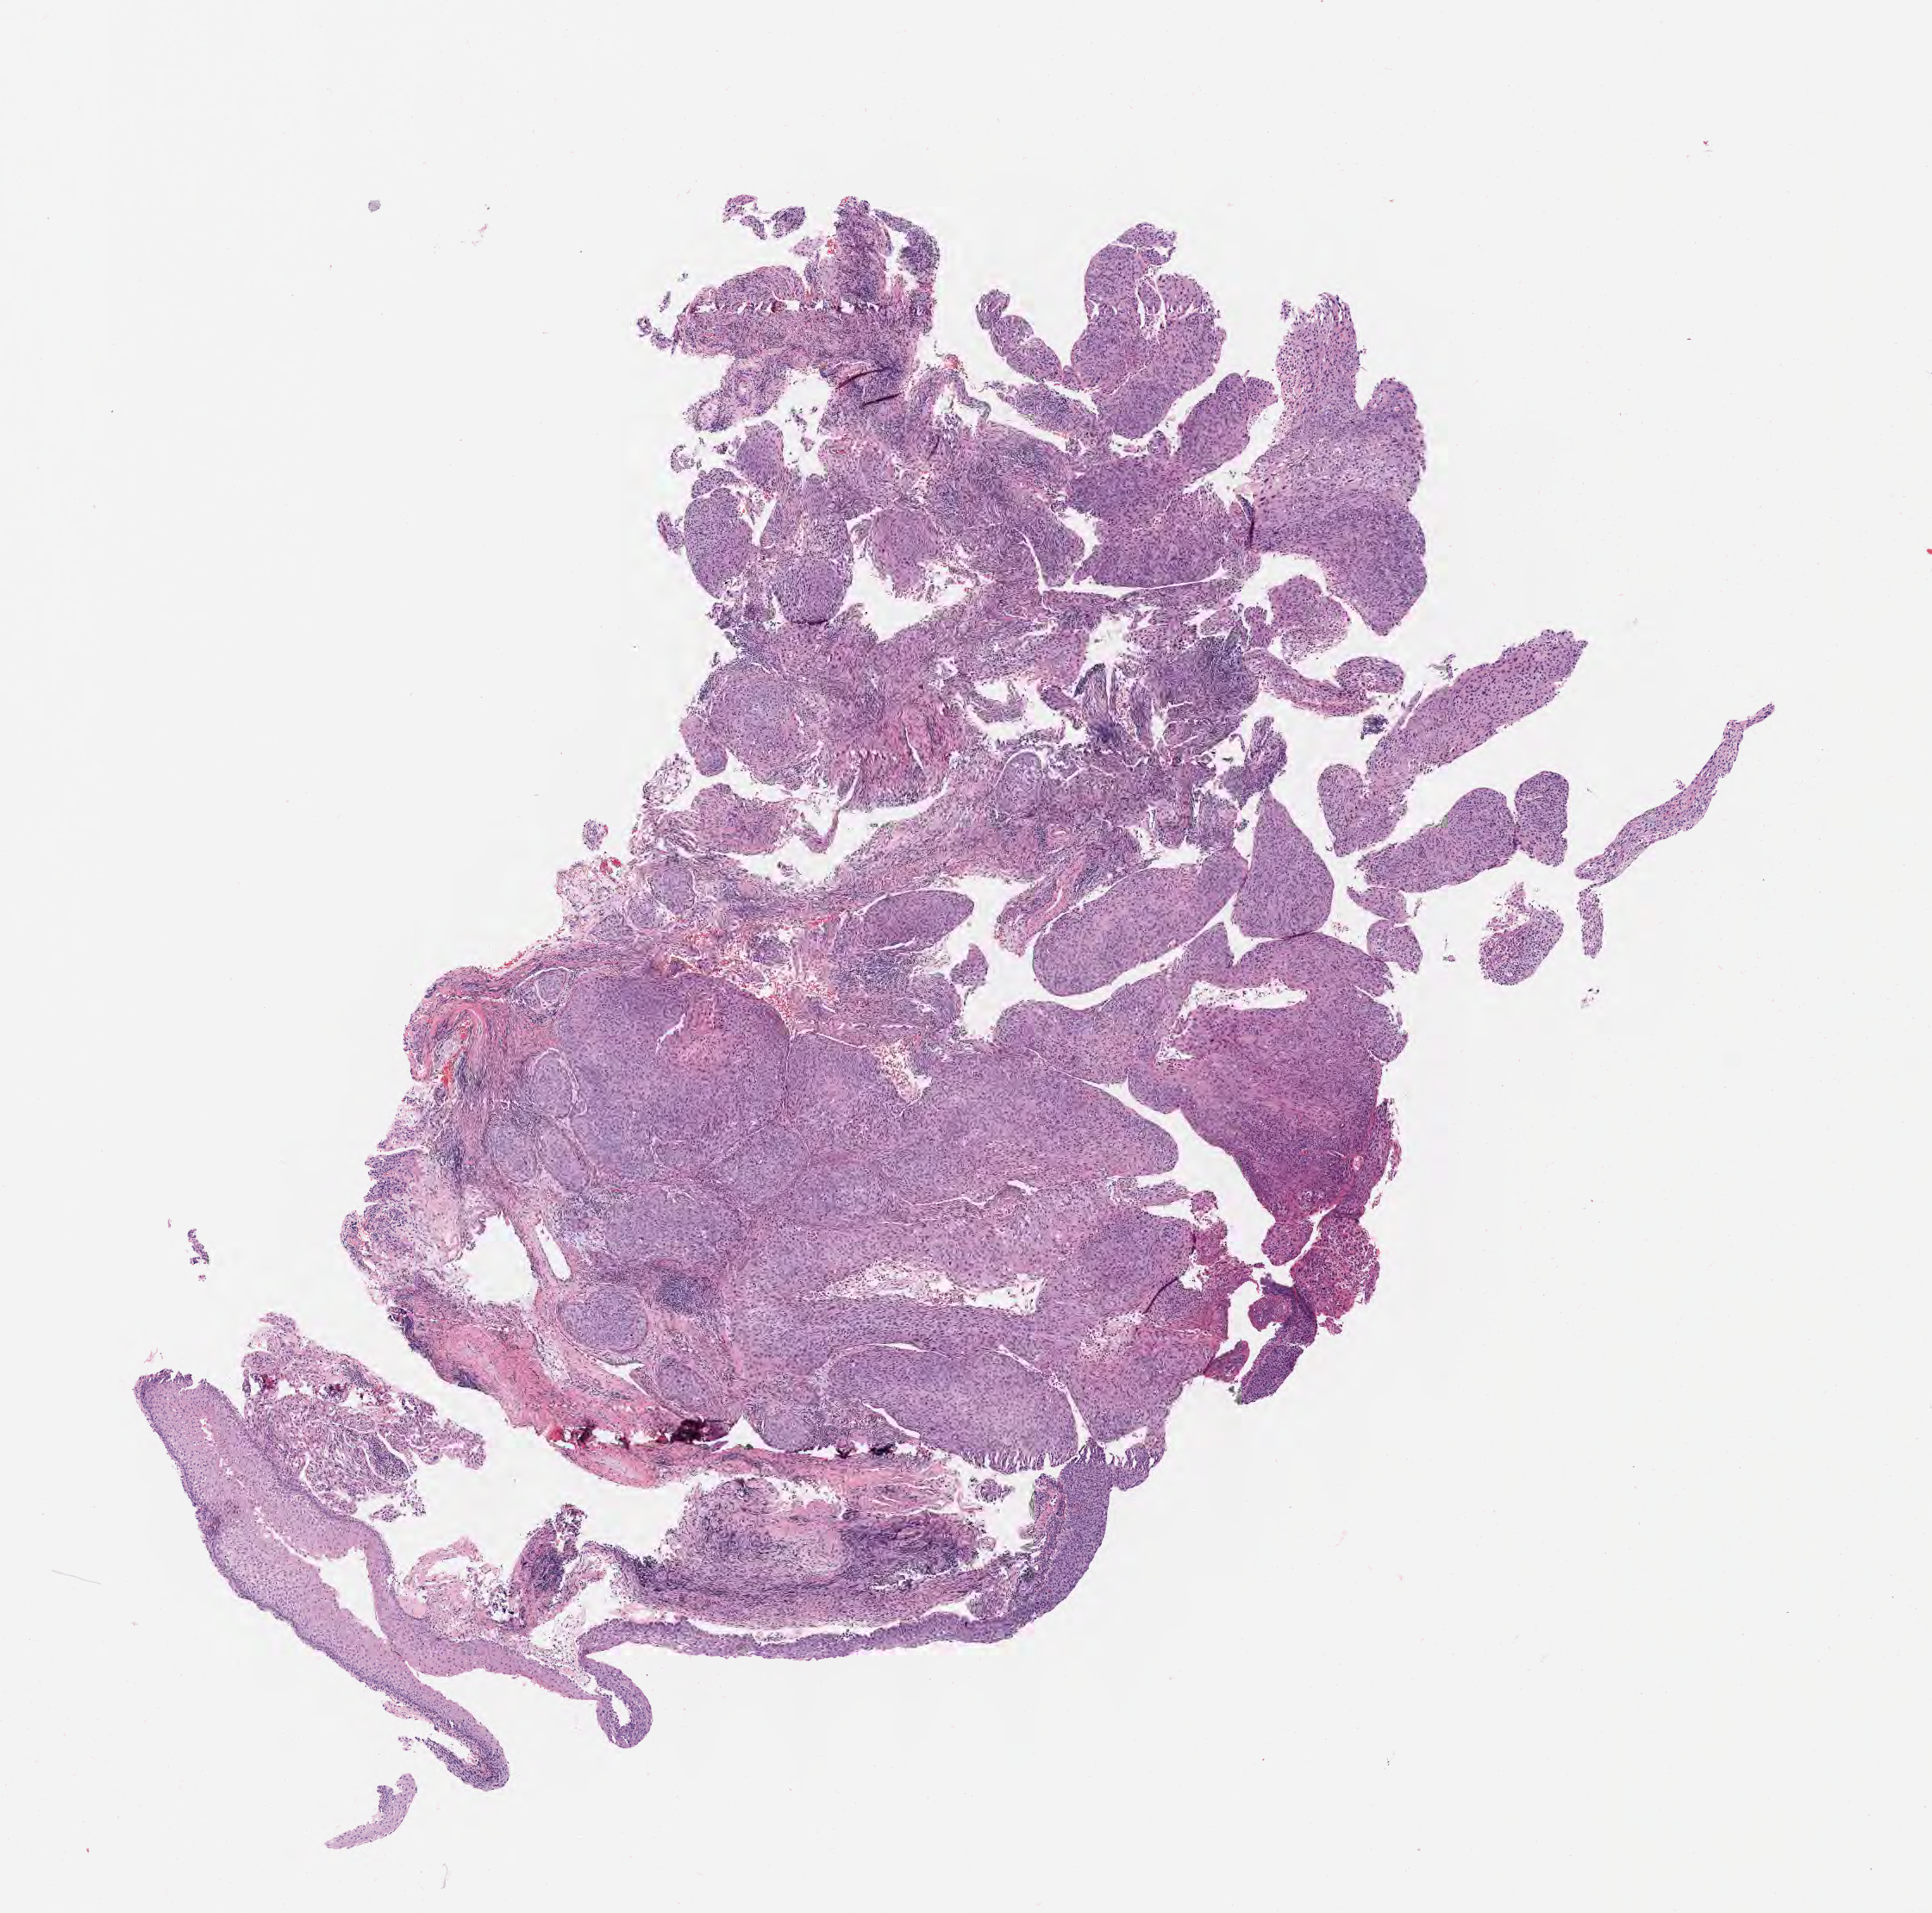
Whole-slide image, hematoxylin and eosin (H&E) stain, low-resolution overview of the scanned area, about 9.1 x 9.0 mm, specimen: tumor tissue, site: cervix. Patient female; aged 82.
Histologic diagnosis: Squamous cell carcinoma, large cell, nonkeratinizing, NOS.